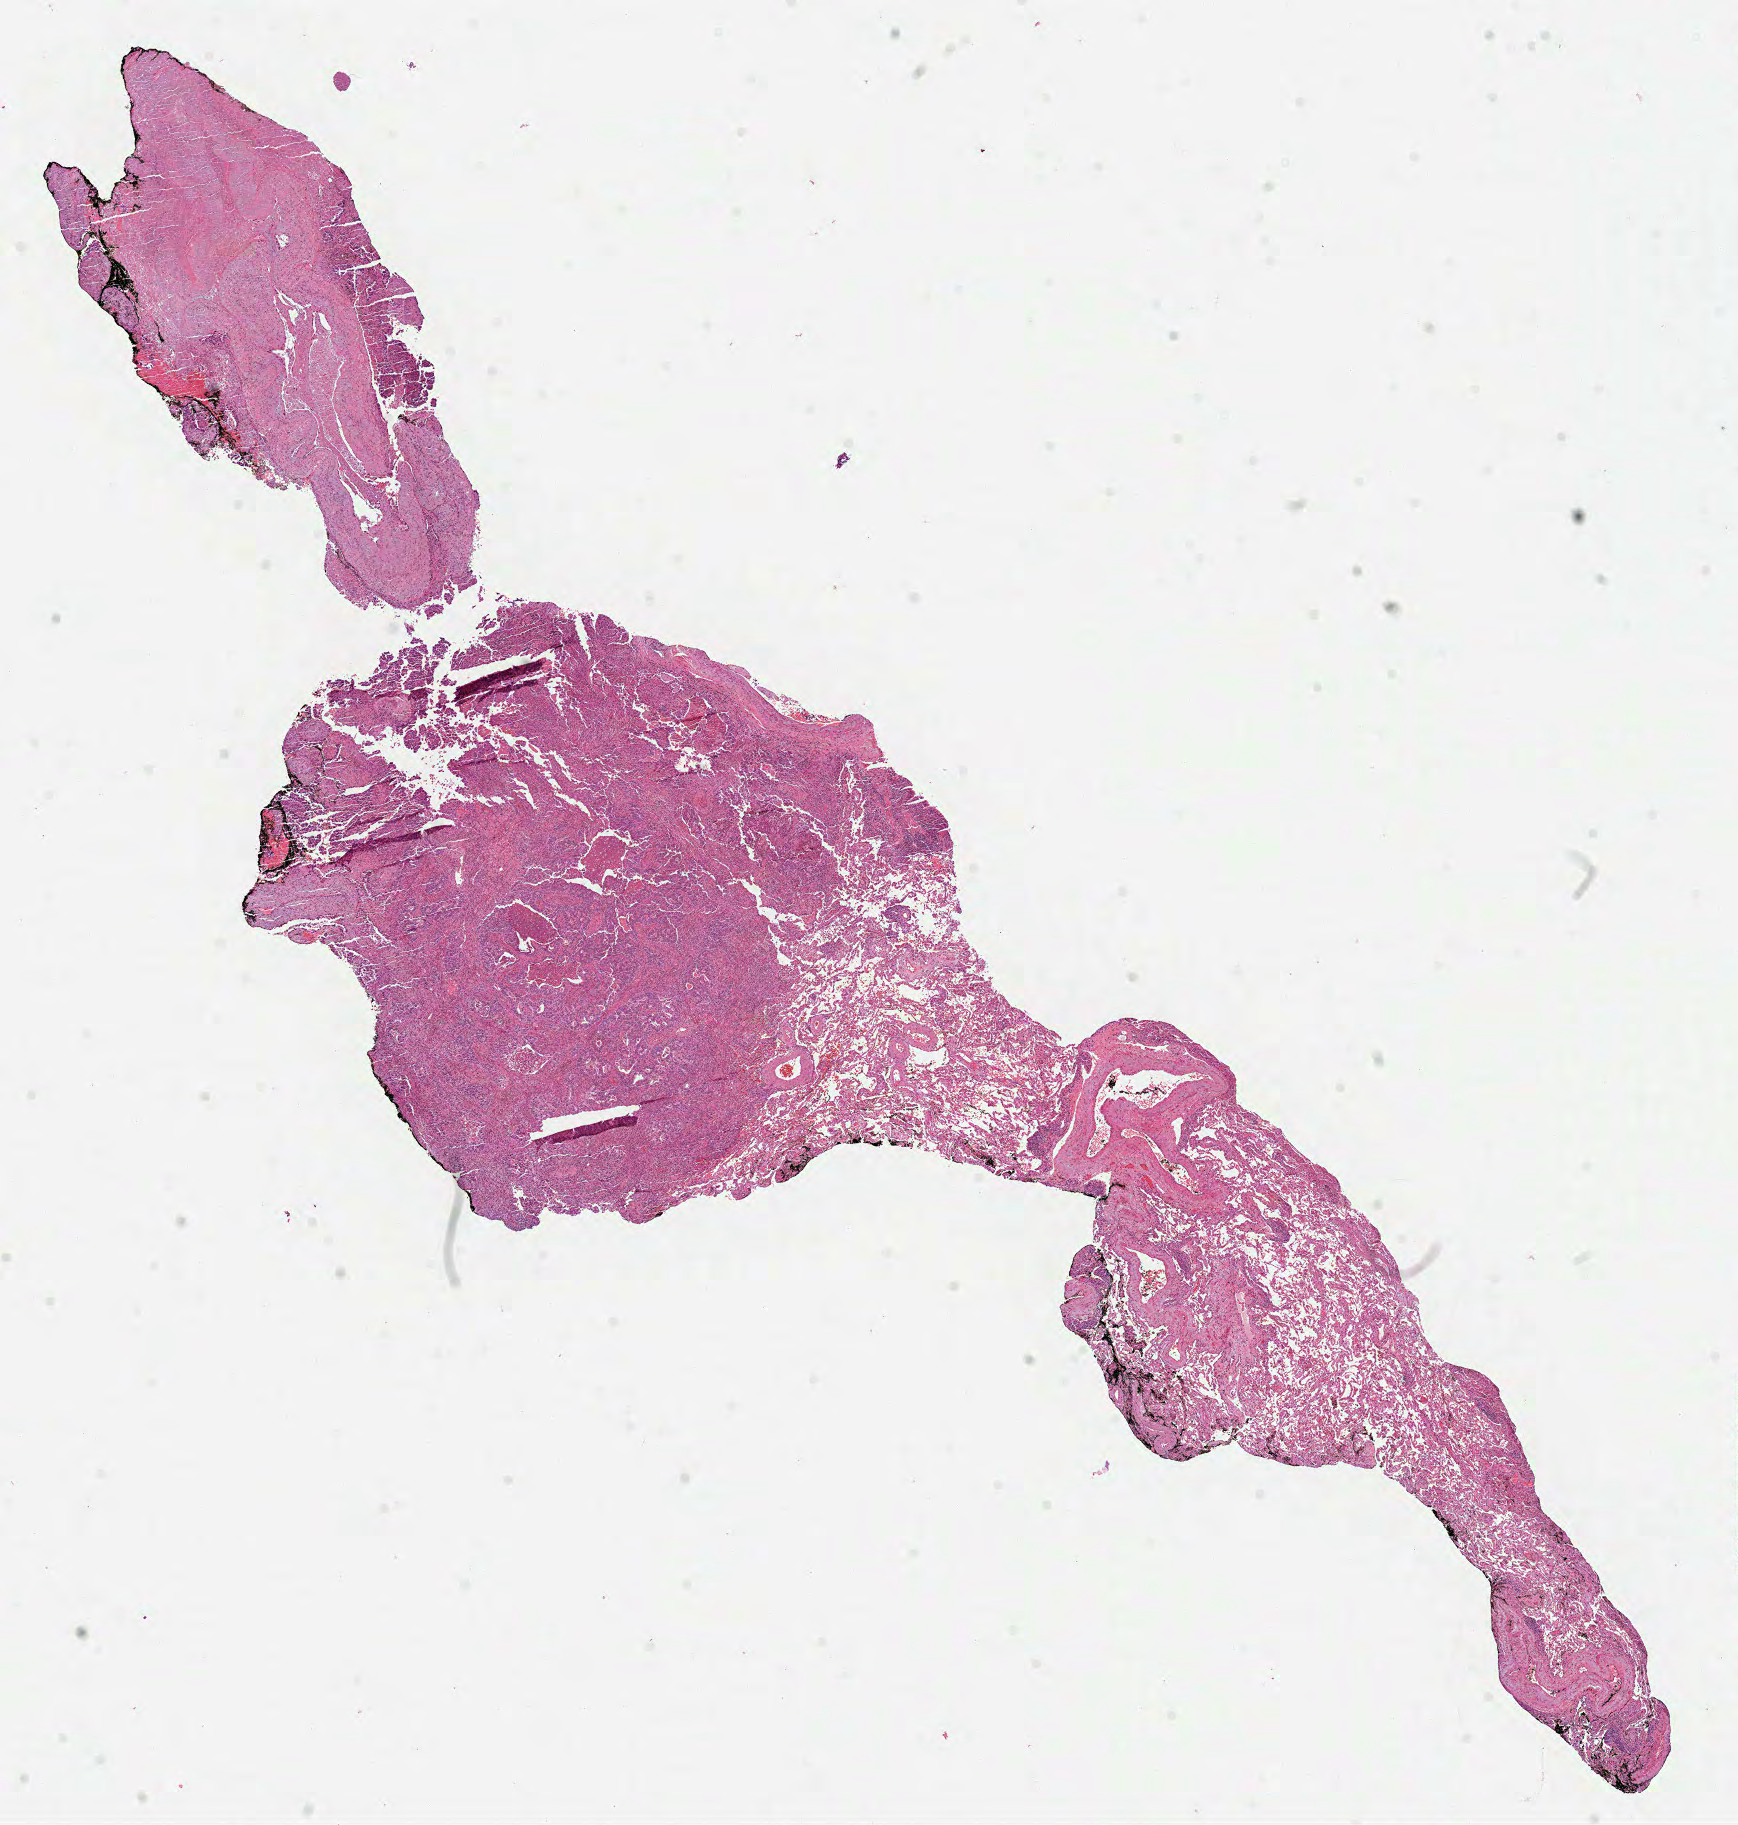
Hematoxylin and eosin (H&E) stained whole-slide image — low-resolution overview of the scanned area, about 14.0 x 14.7 mm (acquisition: 40x scan). FFPE section. Lung, primary tumour sample. Male patient.
* pathologic diagnosis: Adenocarcinoma, NOS (lower lobe, lung)
* AJCC pathologic stage: IA